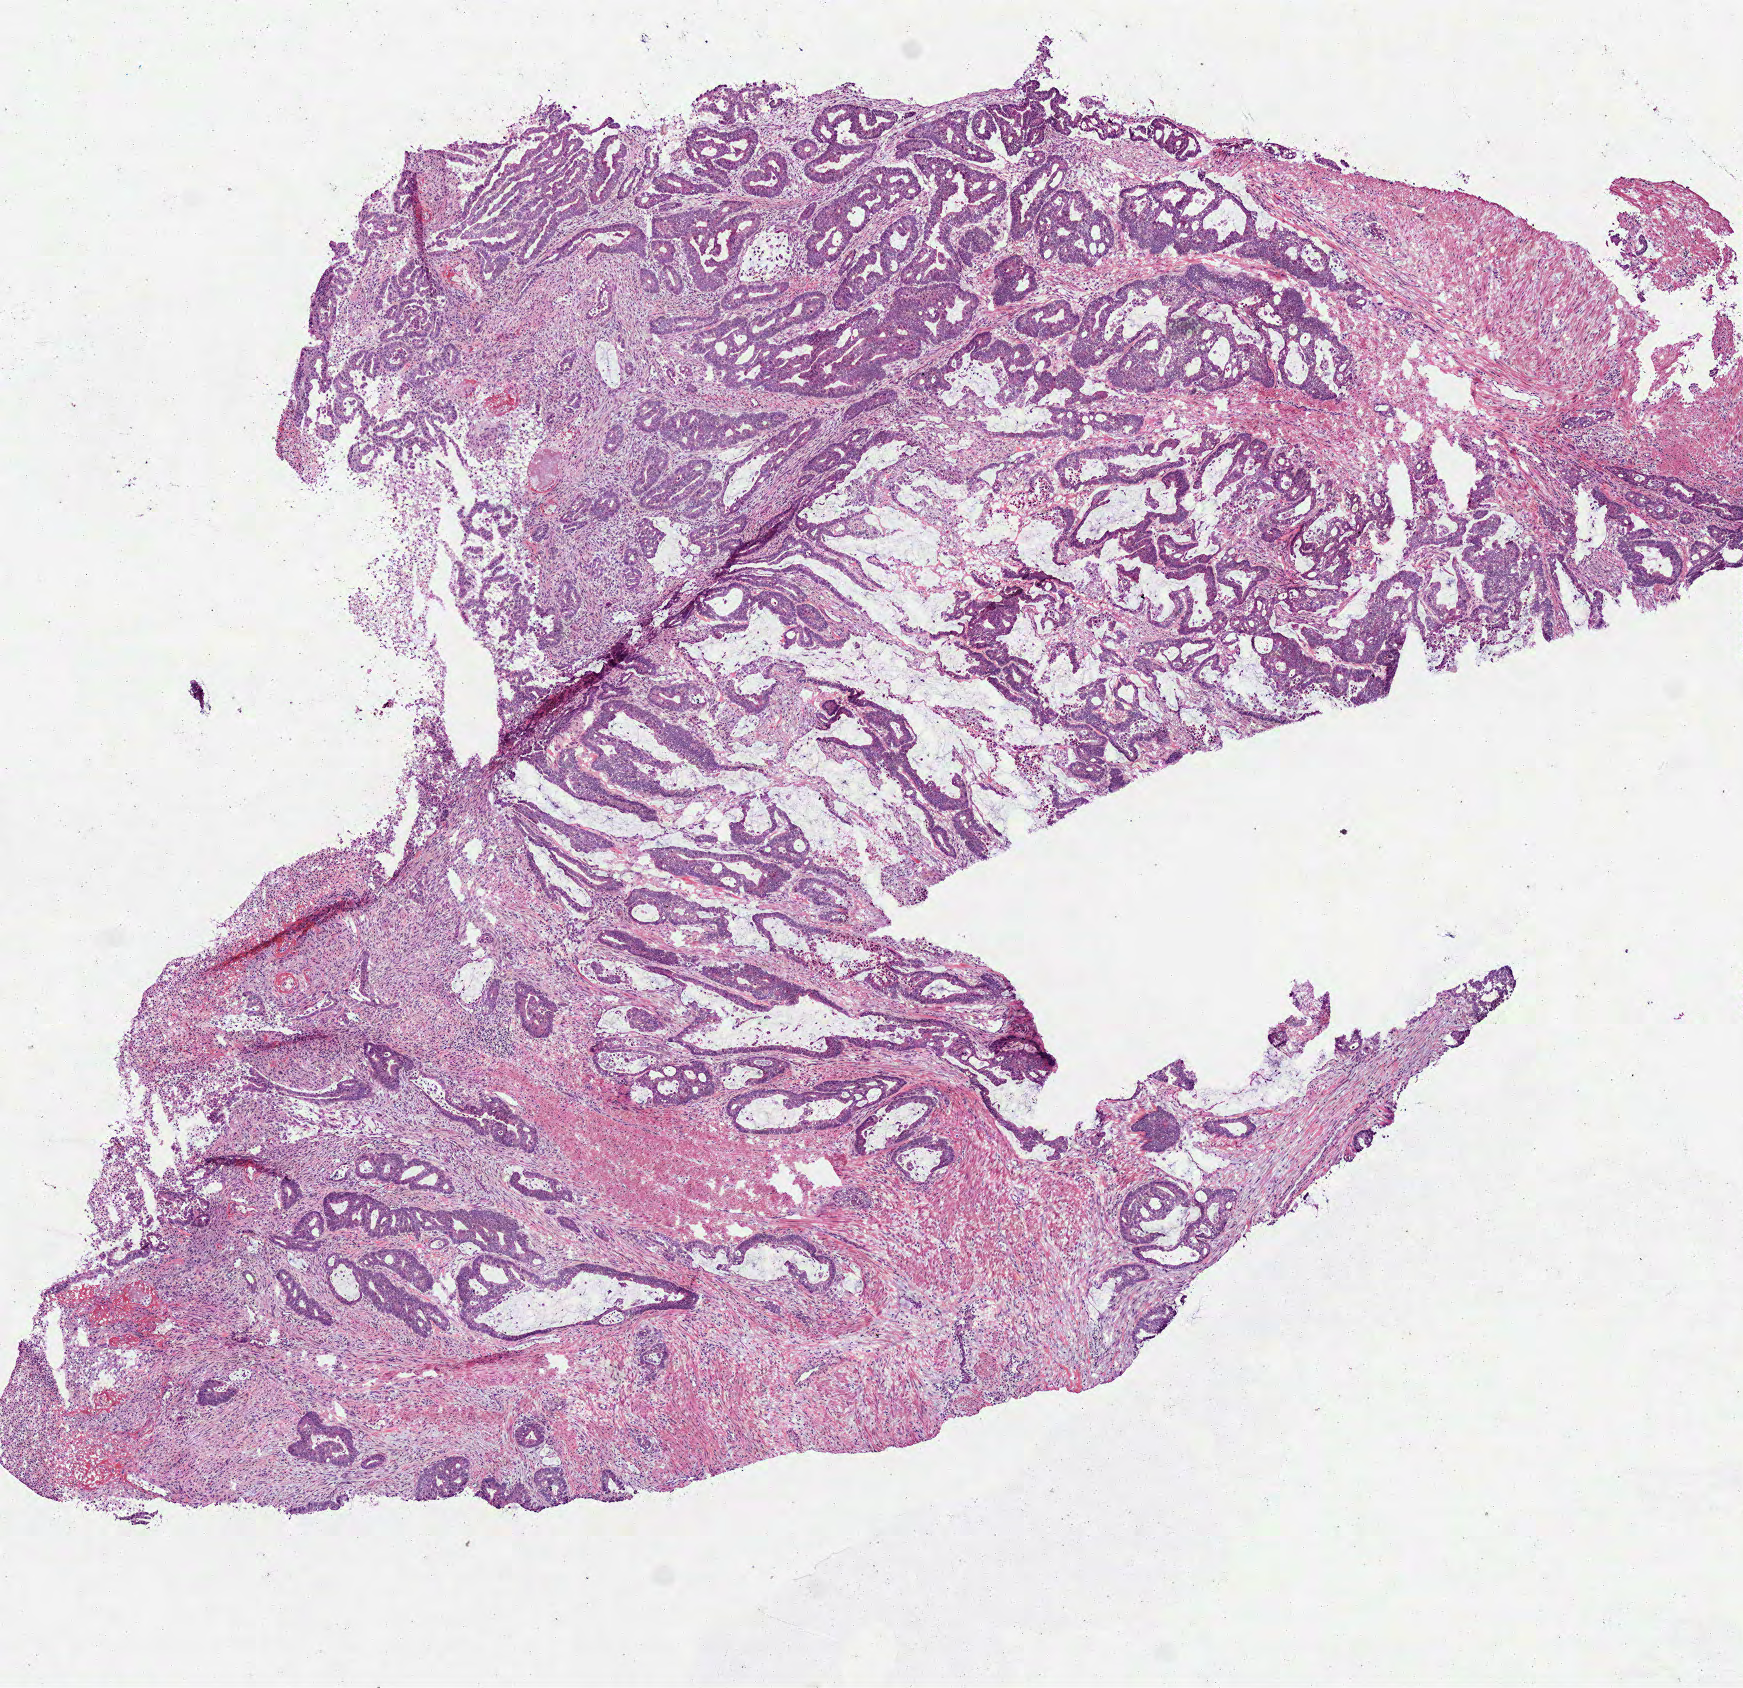
H&E whole-slide image, a low-resolution overview of the entire scanned area, about 7.0 x 6.8 mm, frozen section from the bottom of the tissue portion, colon, primary tumour sample. Female patient; age at initial diagnosis 45 years. Pathologist review of this section (percent, as recorded): tumour cells 75%, tumour nuclei 70%, normal cells 0%, stromal cells 25%, necrosis 0%.
* histologic diagnosis: Mucinous adenocarcinoma (sigmoid colon)
* AJCC pathologic stage: IV